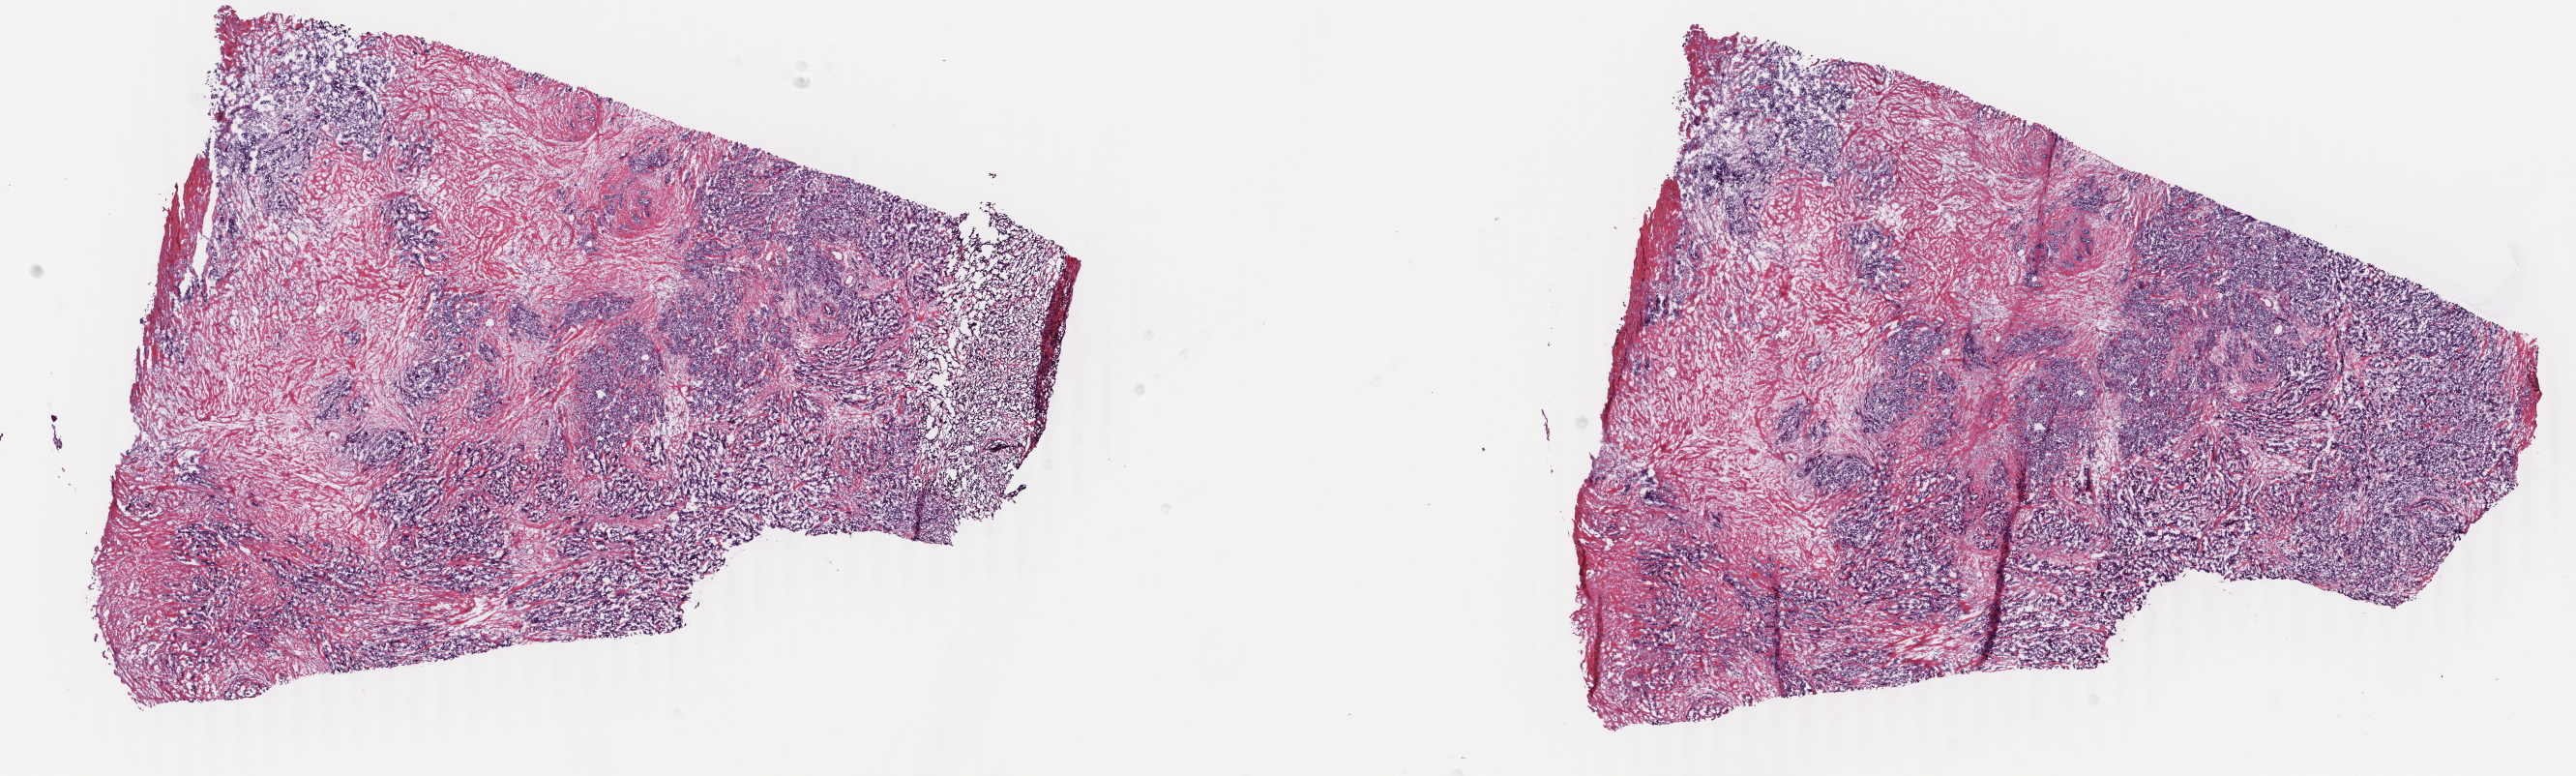
Hematoxylin and eosin (H&E) stained whole-slide image, whole scanned area (about 21.2 x 6.4 mm, slide scanned at 40x) shown as a low-resolution overview. Frozen section from the bottom of the tissue portion. Sample: primary tumour, breast. Female patient; age at initial diagnosis 58 years. Slide review estimates, as recorded: tumour cells 60%, tumour nuclei 70%, normal cells 0%, stromal cells 40%, necrosis 0%. Inflammatory infiltration, as recorded: lymphocyte infiltration 0%, monocyte infiltration 0%, neutrophil infiltration 0%.
* laterality: right
* lymph nodes positive (case pathology): 0 of 12 examined
* AJCC pathologic stage: IIA (7th edition)
* diagnosis: Infiltrating duct carcinoma, NOS